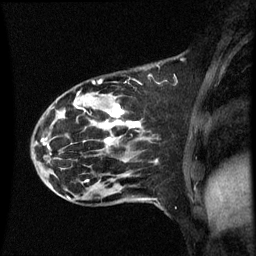
Breast MRI (dynamic contrast-enhanced), one sagittal slice. Position 20 of 60 along the scan axis. Dynamic contrast-enhanced series, image 2 of 3 at this slice position (ordered by acquisition). 1.5 T. TE 4.2 ms, TR 8.9 ms. 2 mm slice thickness. 256 × 256 image matrix, field of view 200 × 200 mm. Patient: female, 44 years. From the clinical record (not read from this slice): setting: breast cancer imaged before/during neoadjuvant chemotherapy; receptor status: HR-positive, HER2-negative.
Structures marked on this image (semi-automatically segmented with operator editing):
- analysis volume of interest (the breast-tissue region the enhancement analysis was run in; not a lesion): box from (x=43, y=80) to (x=153, y=189) px
- tumour enhancement mask (voxels above the 70 % enhancement threshold inside the analysis volume of interest): (x=76, y=106)–(x=140, y=145)